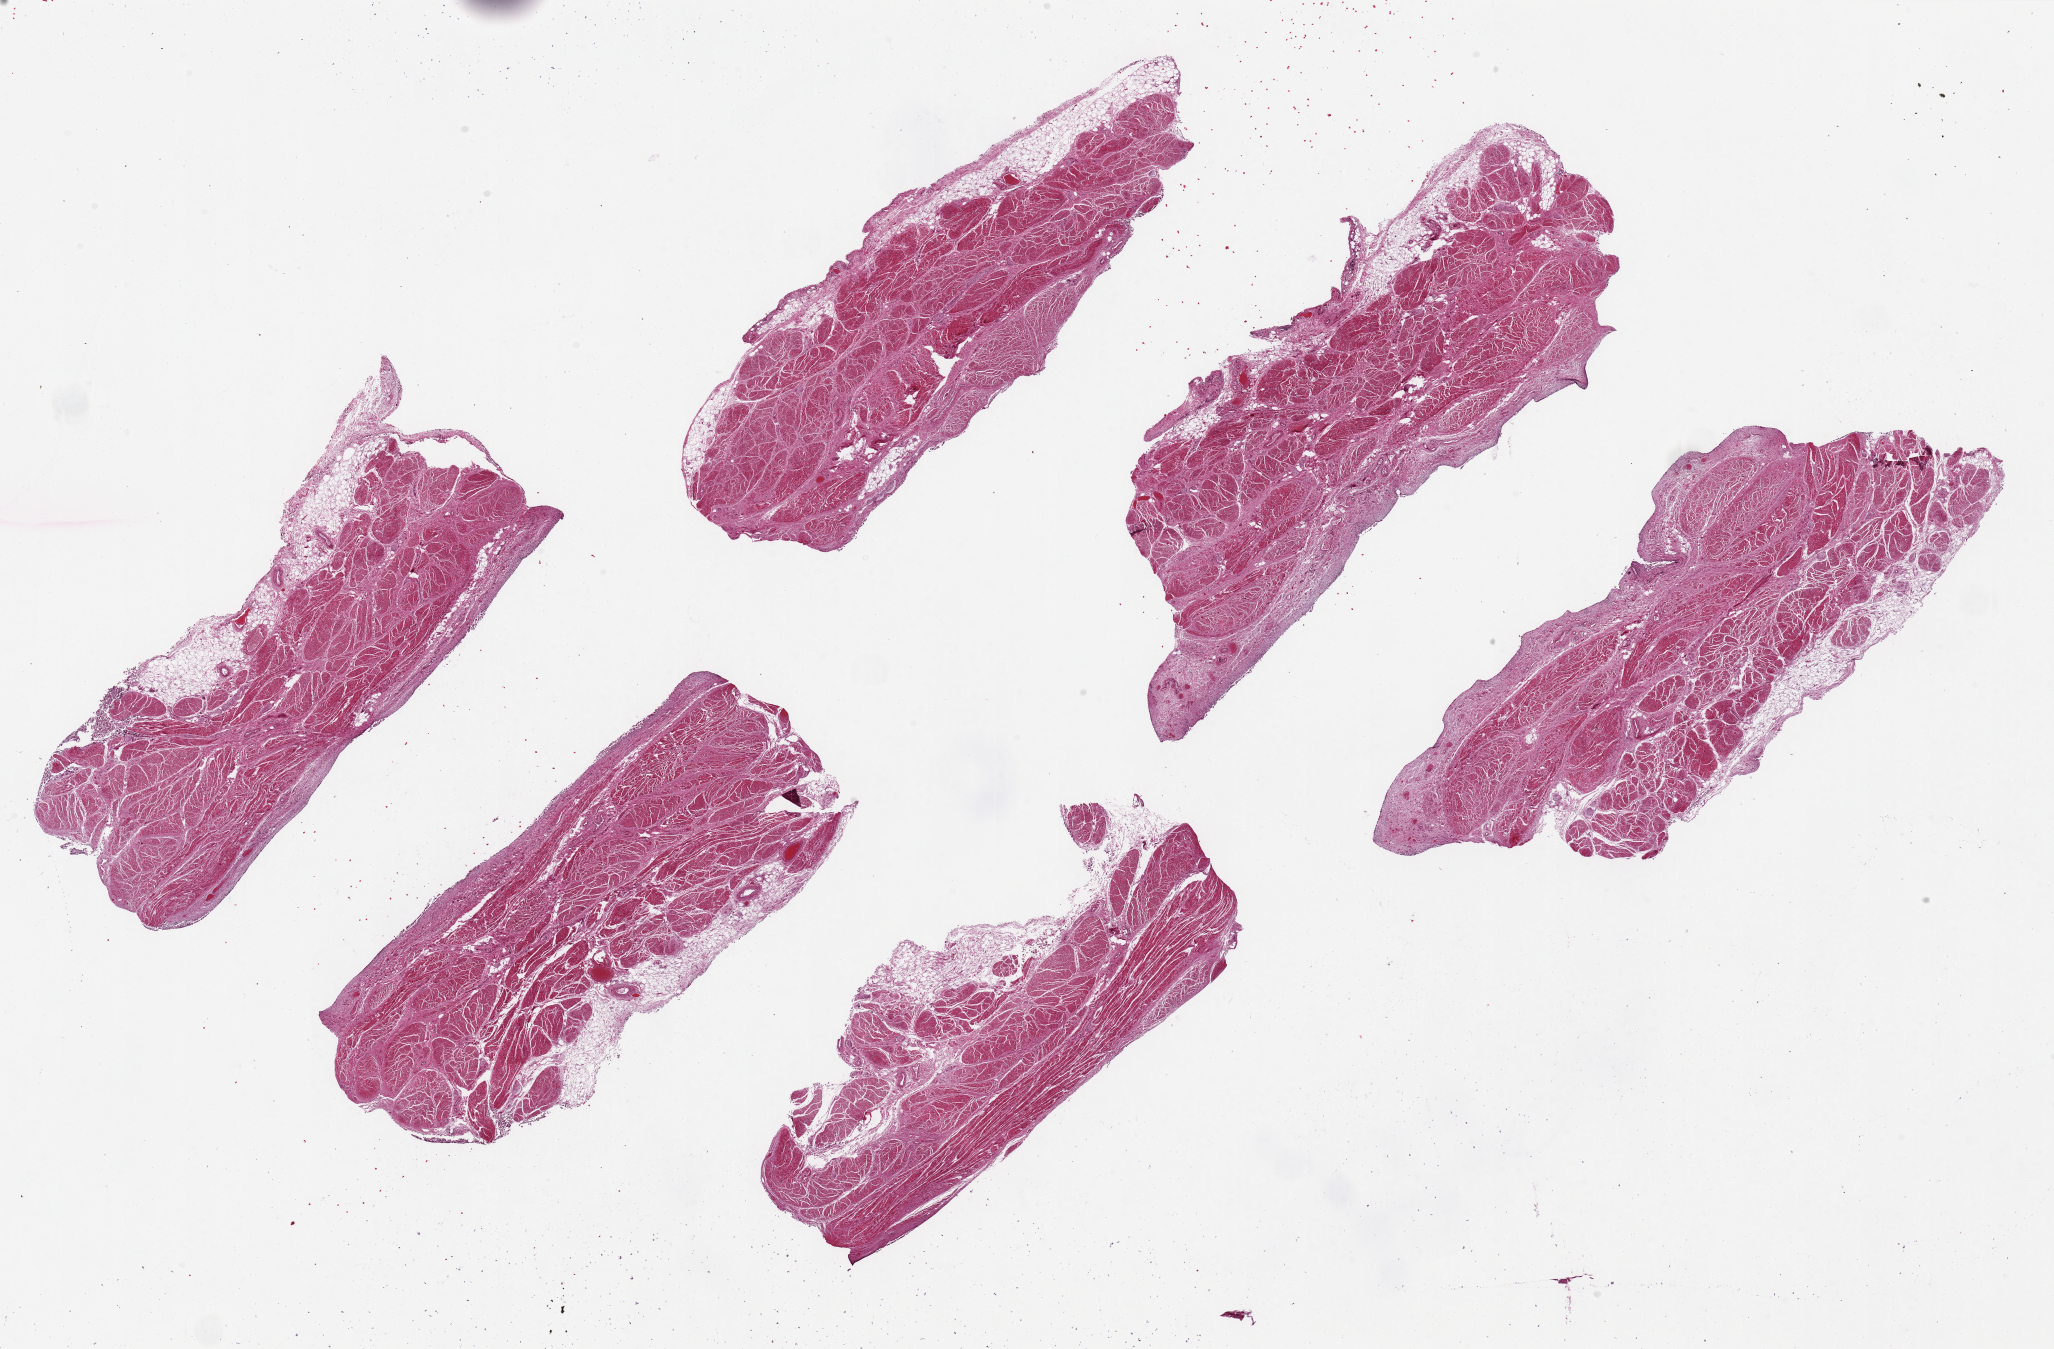
Whole-slide image, hematoxylin and eosin (H&E) stain, low-resolution overview of the scanned area, about 32.5 x 21.3 mm (acquisition: 20x scan), PAXgene-fixed, paraffin-embedded tissue, target tissue: urinary bladder, tissue donor sample. Donor: female.
Reviewer comment on this tissue sample: 6 pieces up to 10x4 mm; mucosa completely sloughed, muscularis slight to moderate autolysis.